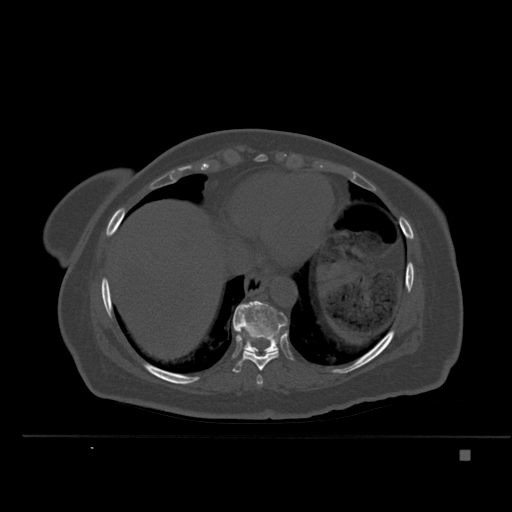
CT including the spine, one axial slice; slice 293 of 477 in the series (ordered by position); bone window (W 1800 / L 400 HU); 512 × 512 image matrix, field of view 422 × 422 mm. Female patient, age 74 years. Case-level facts recorded for this patient, not image findings: primary cancer: colon.
Structures marked on this image (semi-automatic segmentation, software-assisted and operator-edited):
- T10 vertebra: bounding box [x1, y1, x2, y2] px = [233, 300, 287, 352]
- T8 vertebra: [256, 375, 263, 386]
- T9 vertebra: [233, 307, 287, 373]